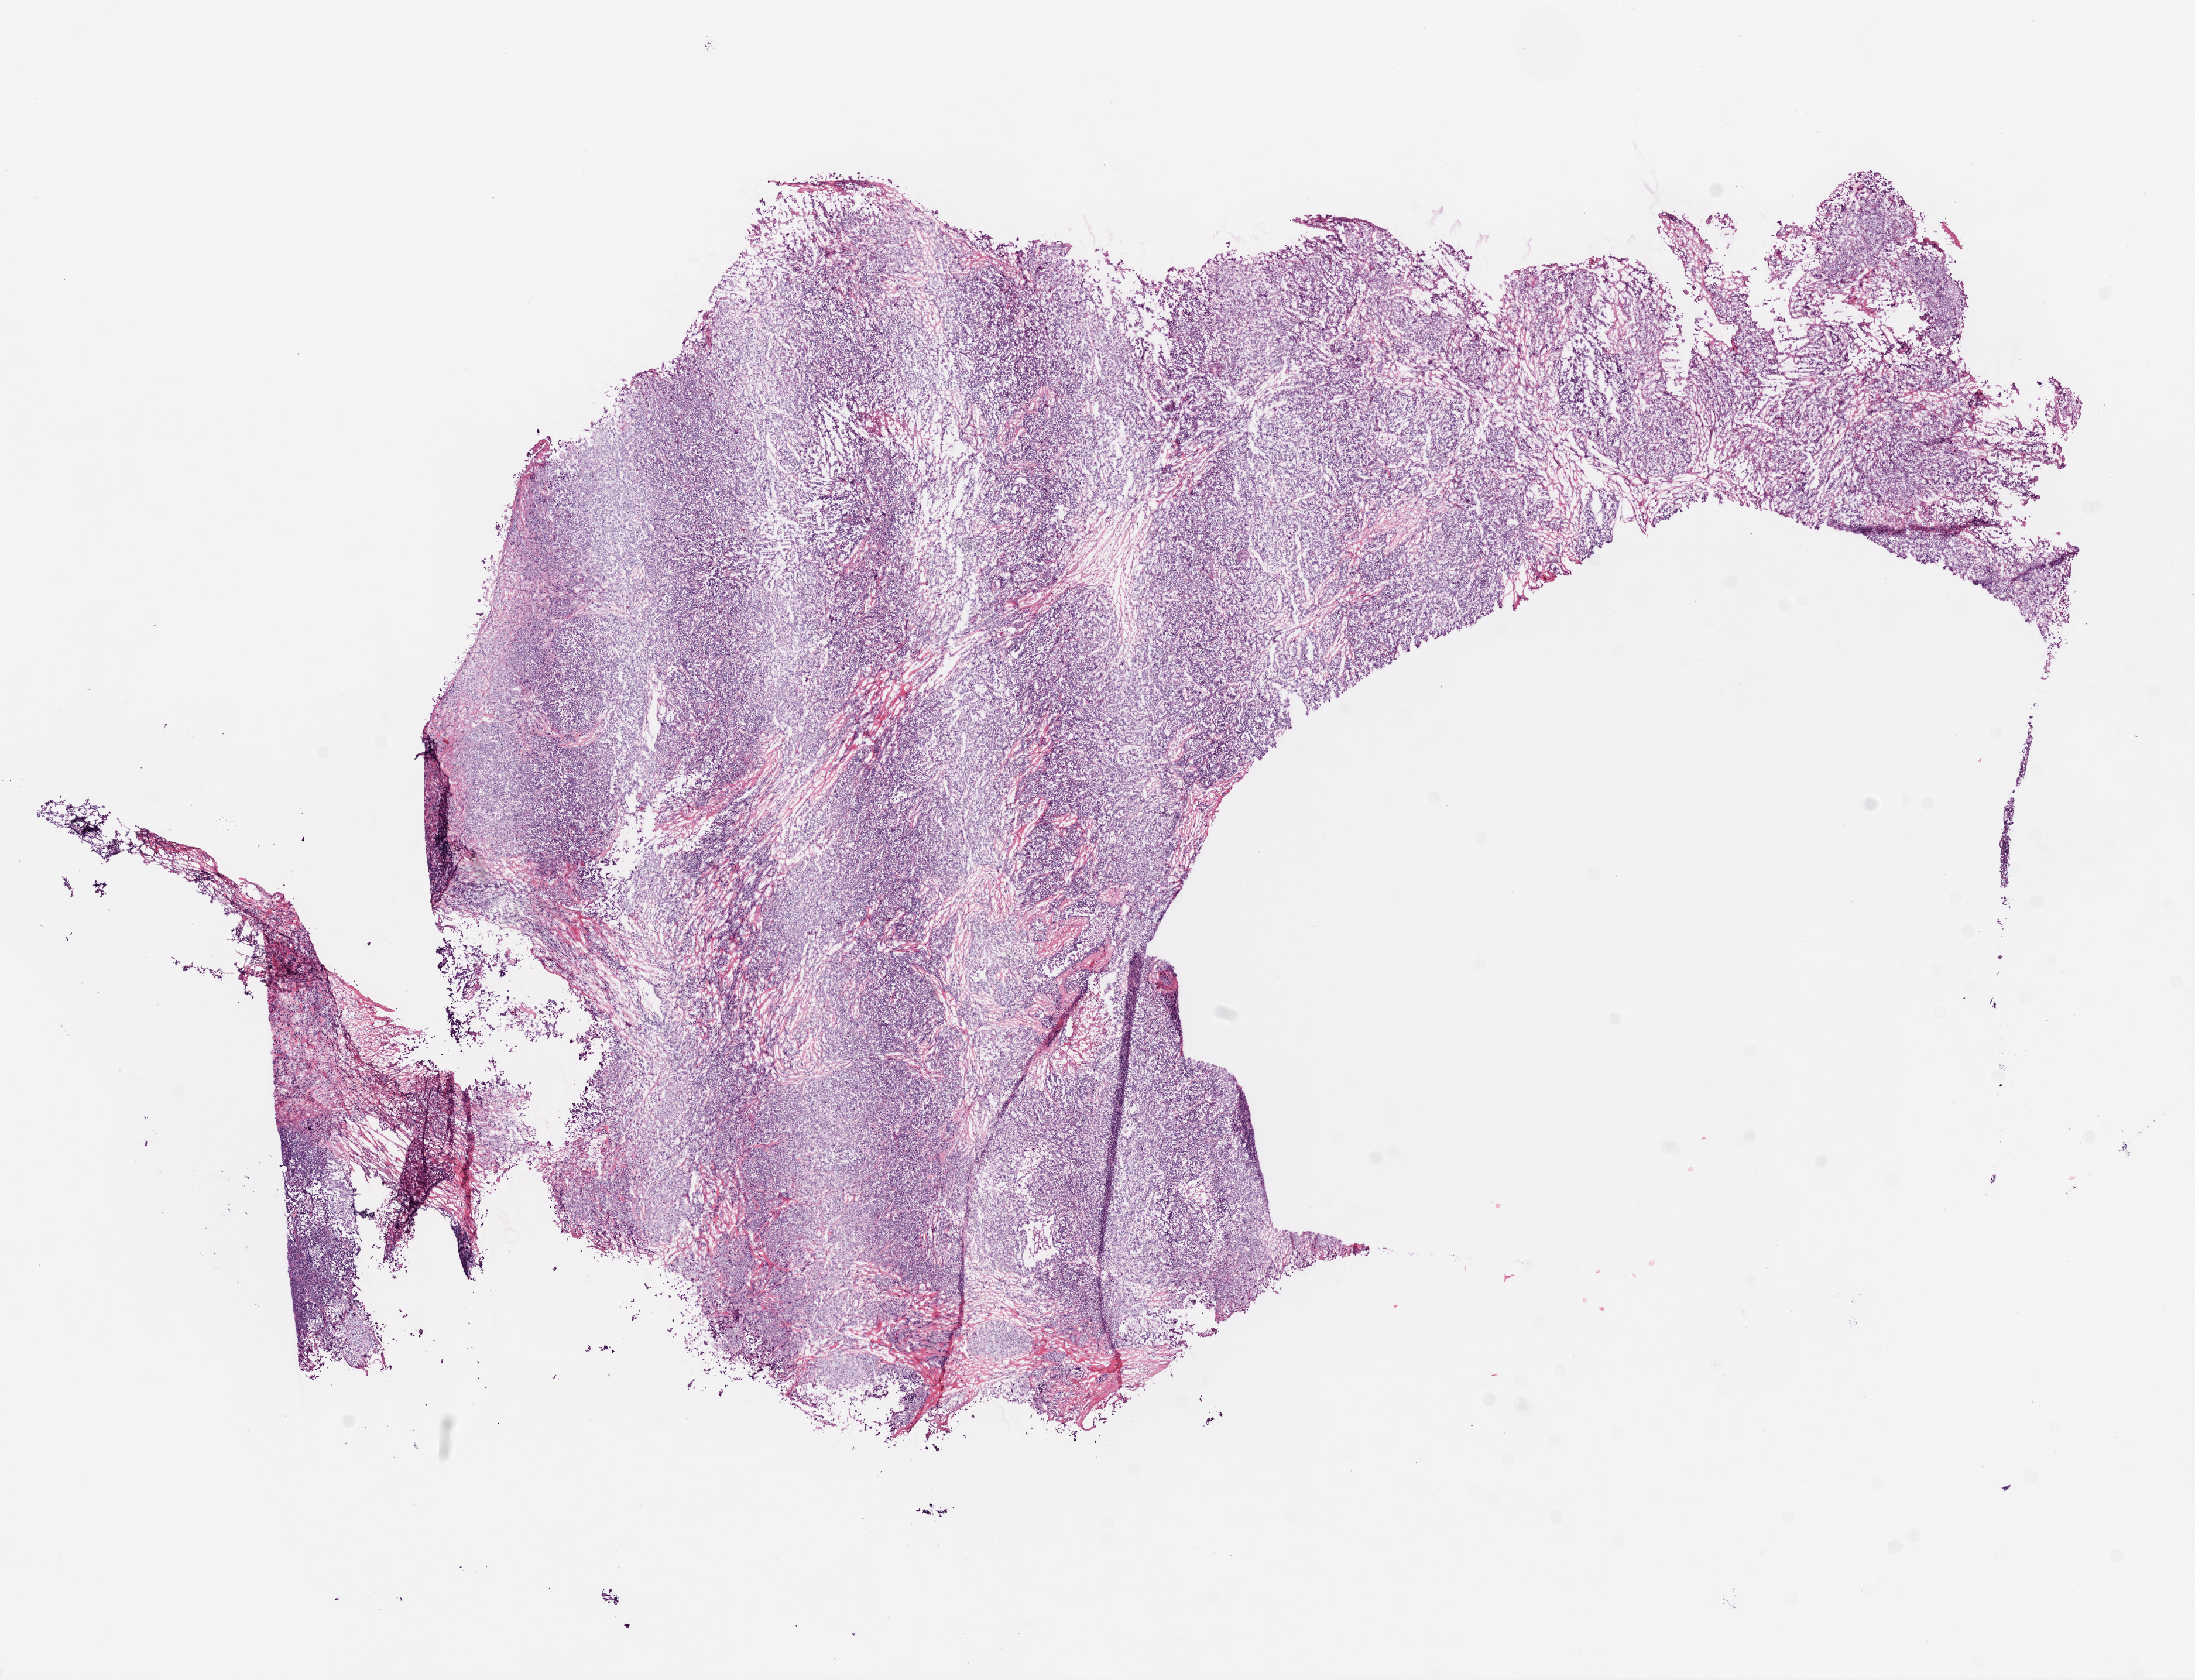
Hematoxylin and eosin (H&E) stained whole-slide image, low-resolution overview of the scanned area, about 15.0 x 11.5 mm (from a 20x scan); frozen section from the bottom of the tissue portion; ovary, primary tumour sample. Patient: female, age at initial diagnosis 78 years. Histologic grade: G3 (poorly differentiated). Slide review estimates, as recorded: tumour cells 95%, tumour nuclei 95%, normal cells 0%, stromal cells 5%, necrosis 0%.
• laterality: left
• diagnosis: Serous cystadenocarcinoma, NOS
• FIGO stage: IV